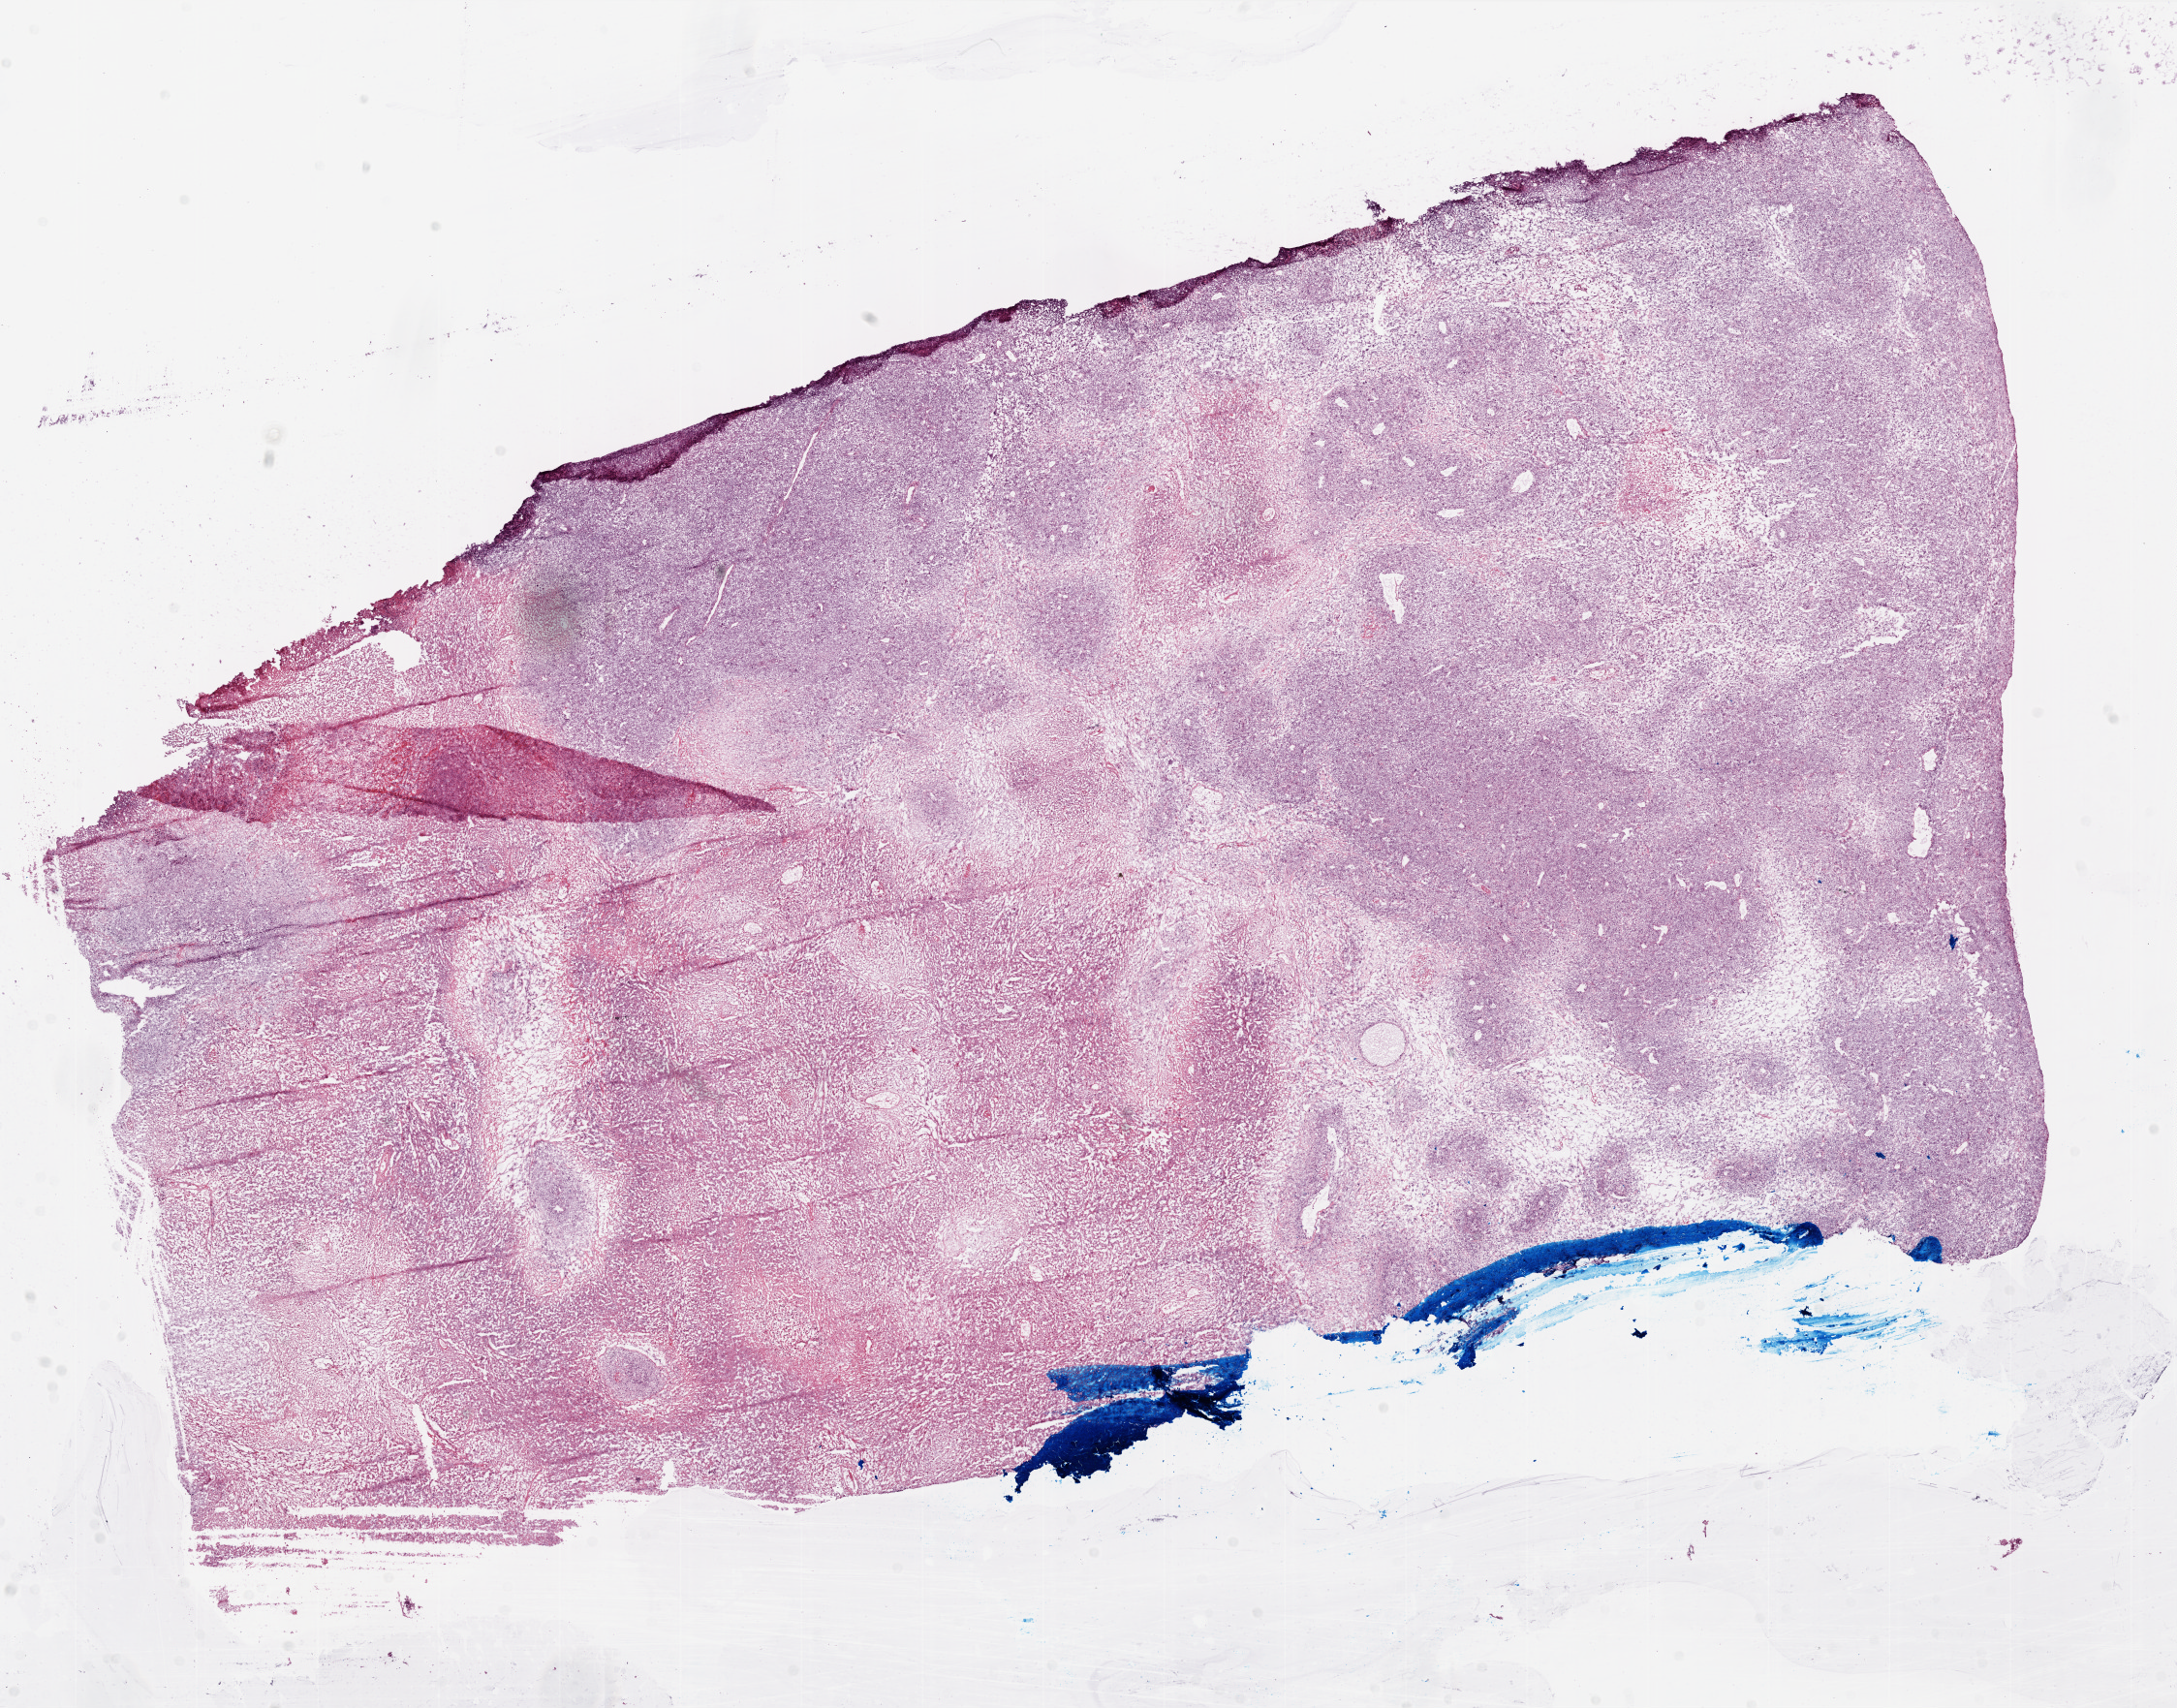
Whole-slide histology image, H&E — shown as a low-resolution overview of the whole scanned area (about 18.0 x 14.1 mm, from a 20x scan). Frozen section from the top of the tissue portion. Sample: primary tumour, brain. Female patient; age at initial diagnosis 67 years. Composition of this section per pathologist review: tumour cells 60%, tumour nuclei 100%, normal cells 0%, stromal cells 0%, necrosis 40%. Infiltration values recorded for this section: lymphocyte infiltration 0%.
- pathologic diagnosis: Glioblastoma